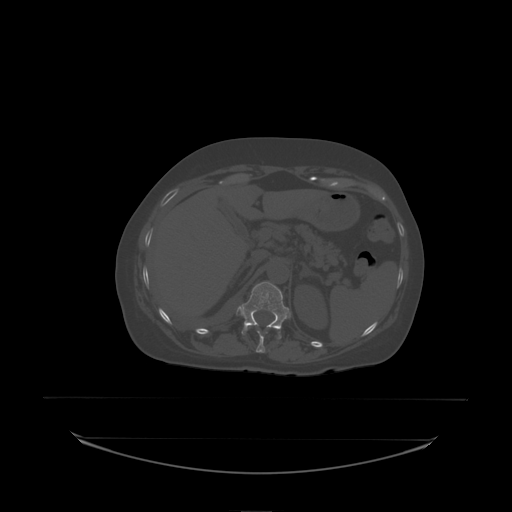
CT including the spine, one axial slice. Position 97 of 242 along the scan axis. Bone window (W 1800 / L 400 HU). 2.5 mm slice thickness. 512 × 512 image matrix, field of view 500 × 500 mm. Female patient, age 53 years. From the clinical record (not read from this slice): primary cancer: lung.
Outlined on this slice (semi-automatic segmentation, software-assisted and operator-edited):
- T11 vertebra: bounding box [x1, y1, x2, y2] px = [258, 332, 264, 338]
- T12 vertebra: [242, 282, 289, 335]